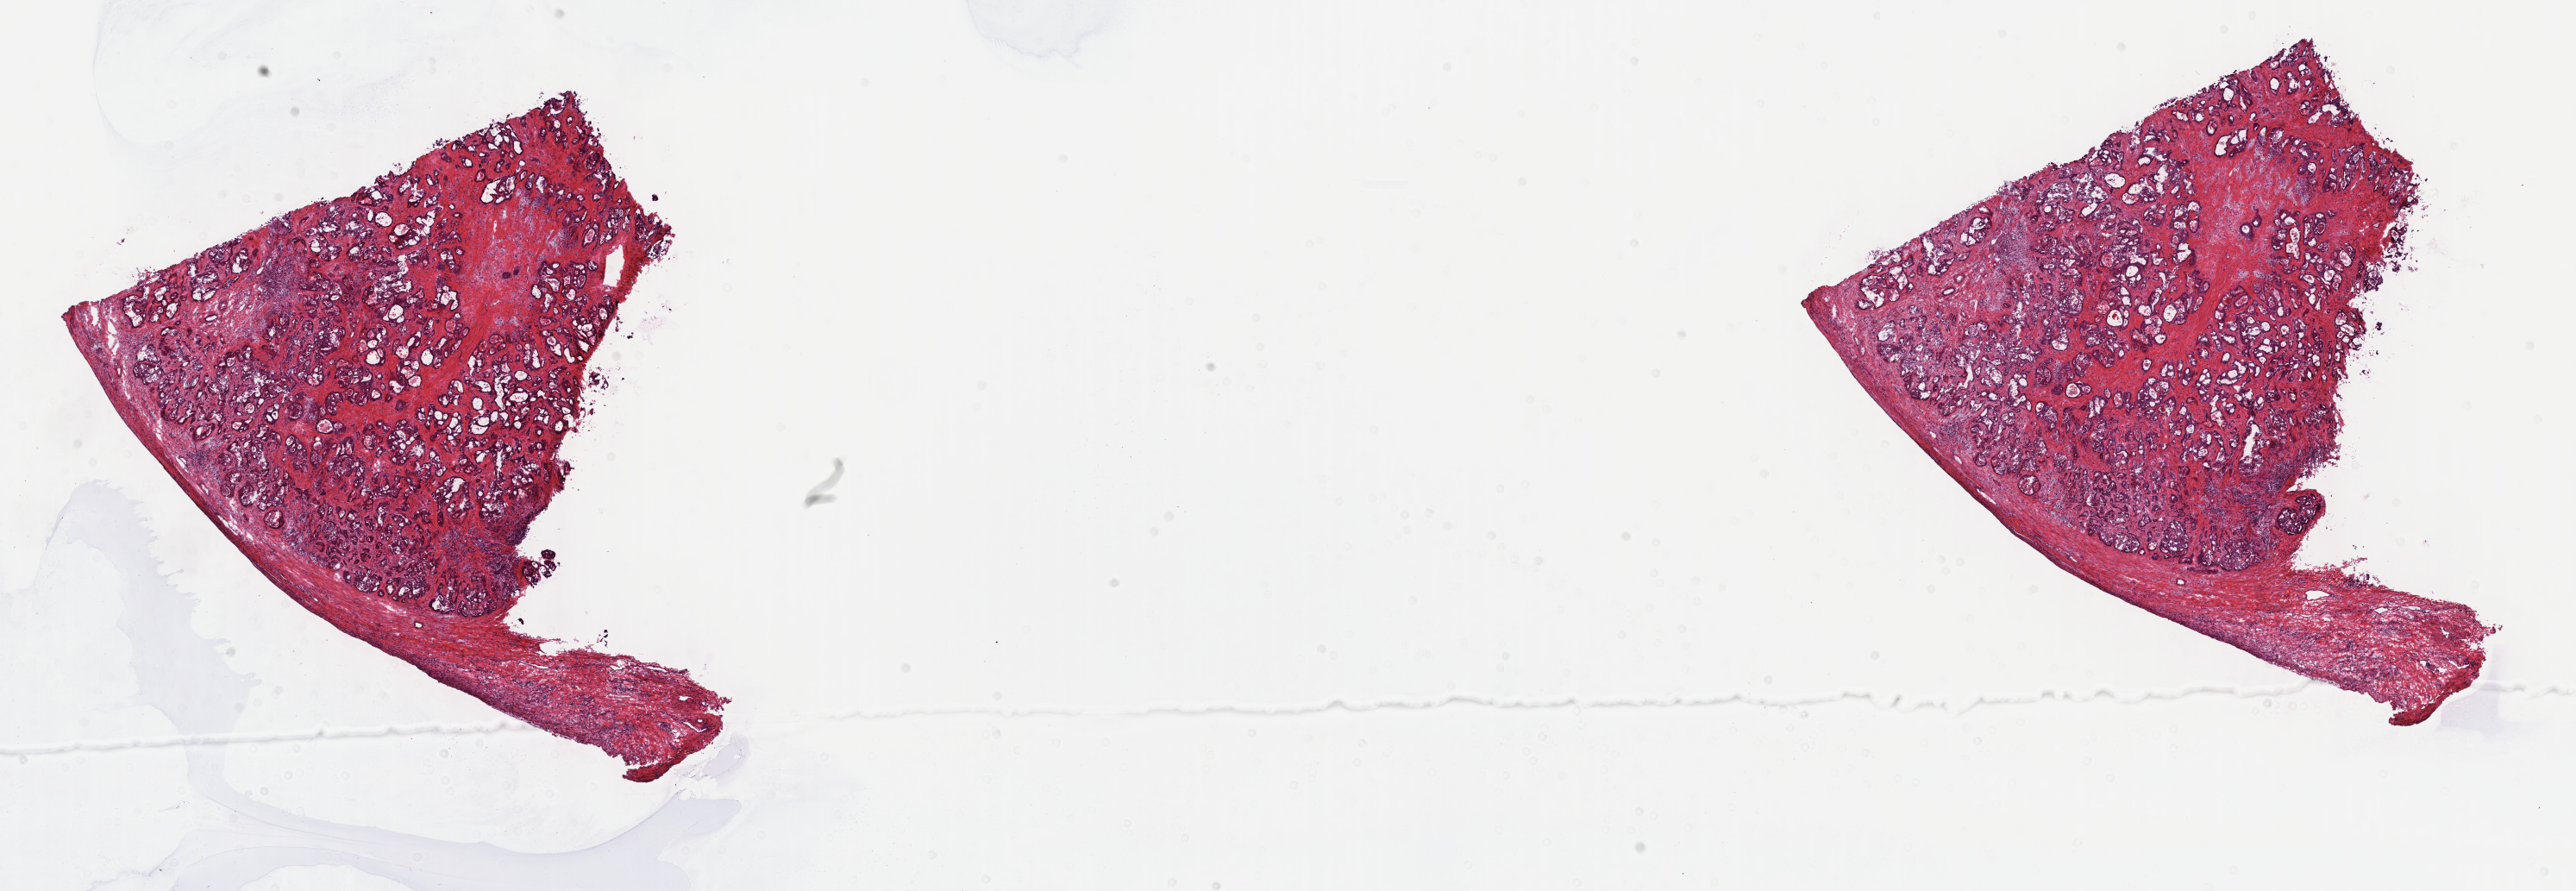
Whole-slide histology image, H&E — low-resolution overview of the scanned area, about 24.2 x 8.4 mm (slide scanned at 40x). Frozen section from the top of the tissue portion. Sample: primary tumour, bile duct. Female patient; age at initial diagnosis 78 years. Histologic grade: G3 (poorly differentiated). Pathologist review of this section (percent, as recorded): tumour cells 80%, tumour nuclei 65%, normal cells 0%, stromal cells 10%, necrosis 10%. Inflammatory infiltration, as recorded: lymphocyte infiltration 0%, monocyte infiltration 0%, neutrophil infiltration 0%.
Diagnosis: Cholangiocarcinoma (intrahepatic bile duct). AJCC pathologic stage: I.